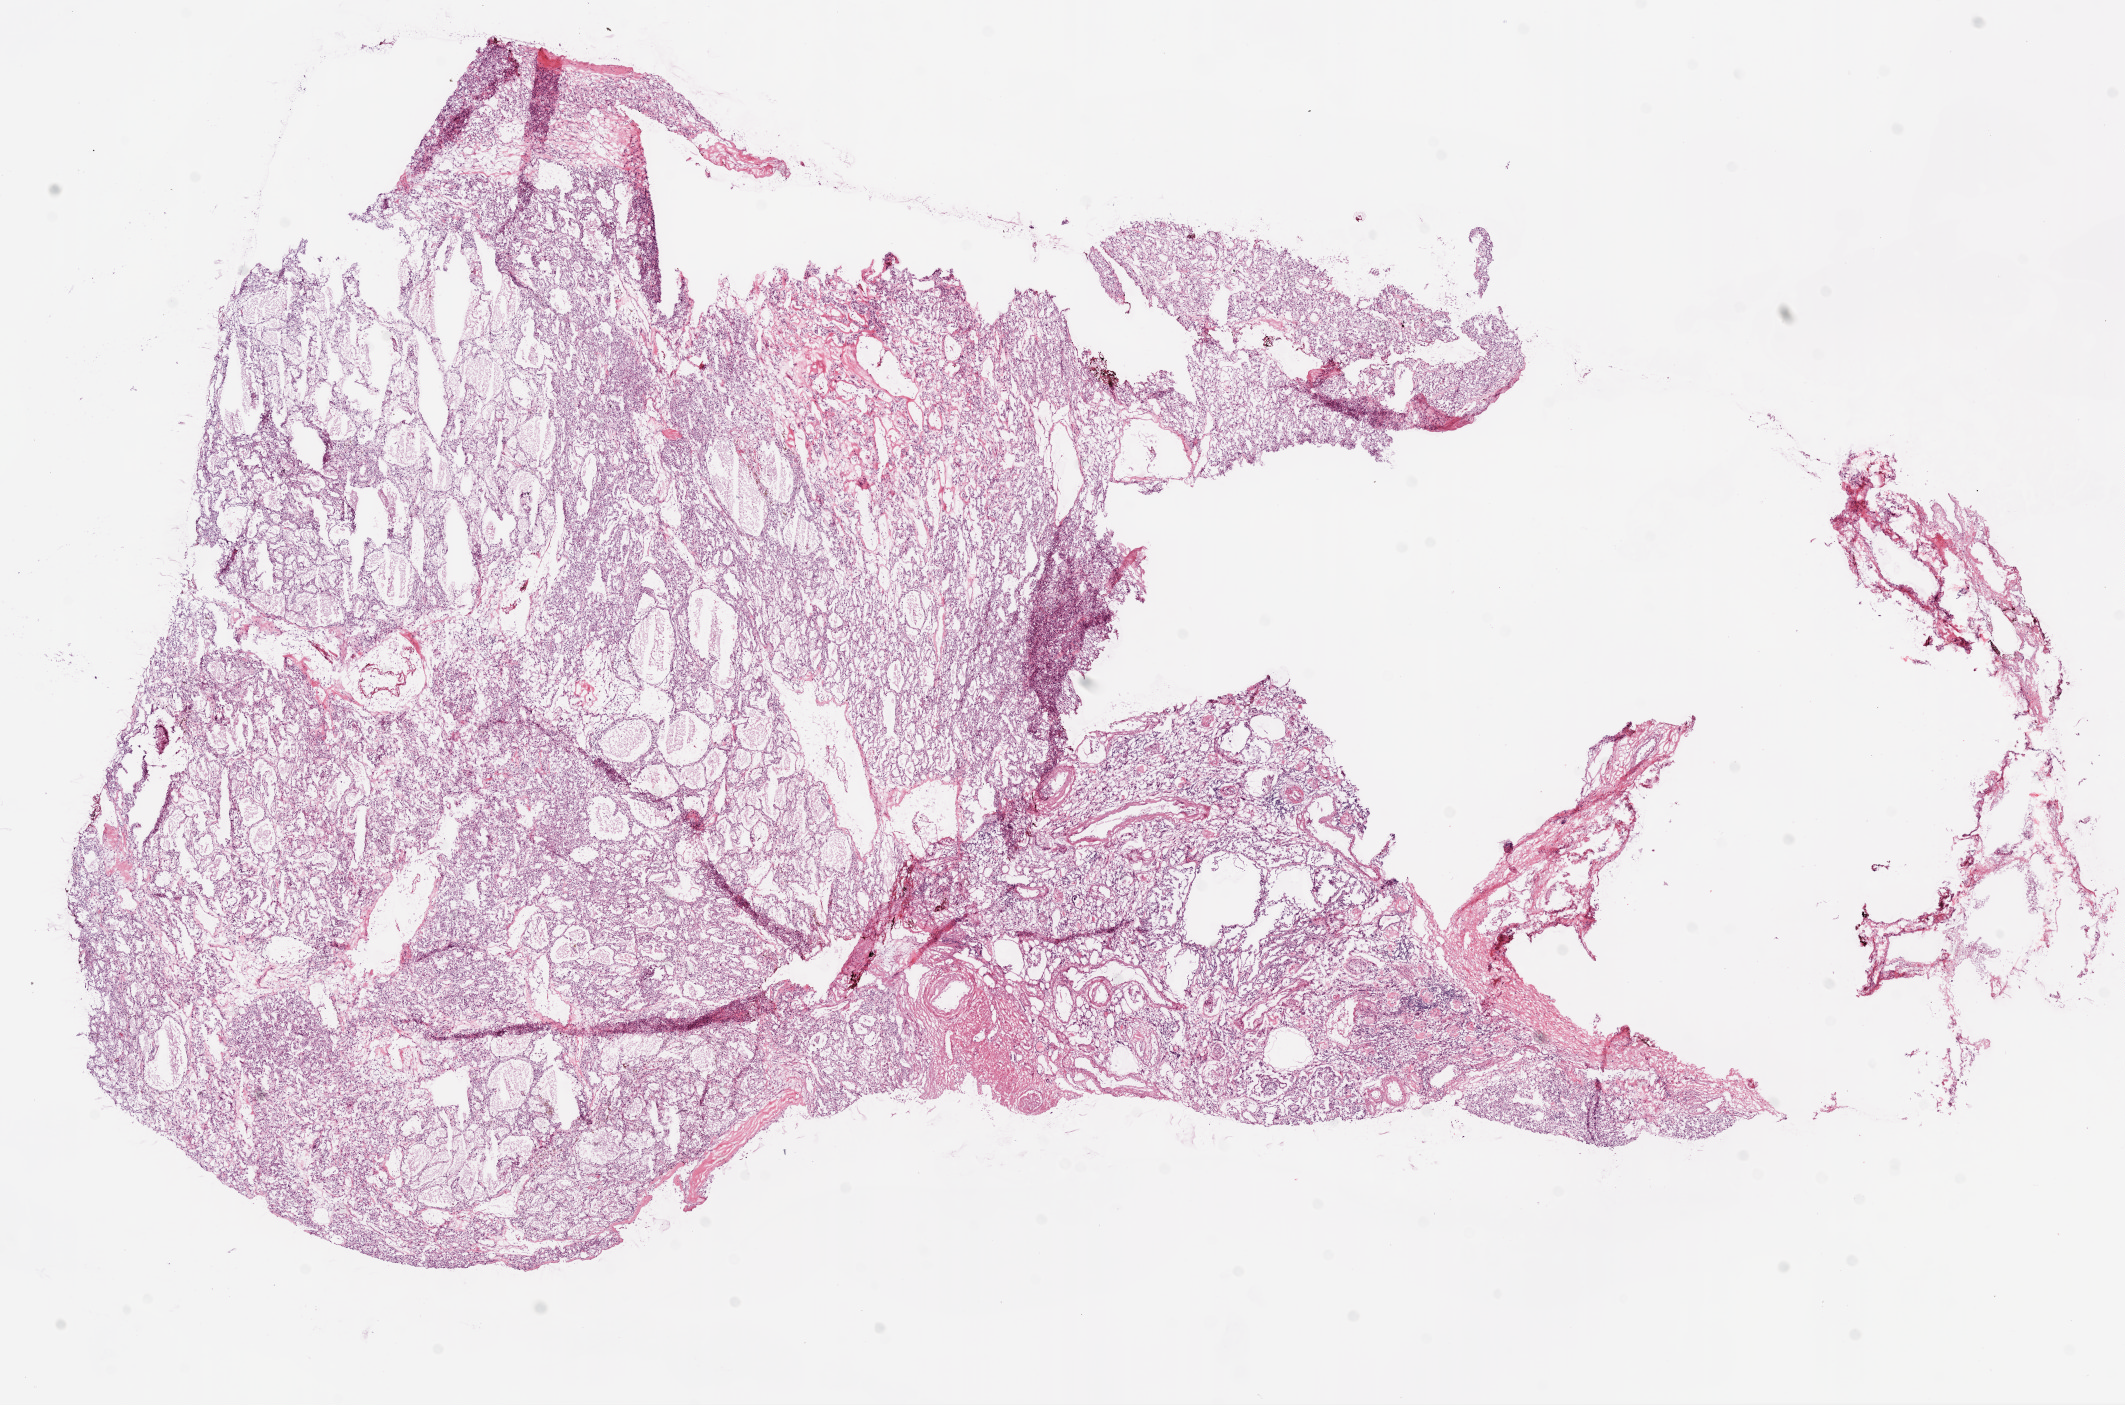
Whole-slide histology image, H&E-stained — low-resolution overview of the scanned area, about 17.1 x 11.3 mm (from a 20x scan), frozen section from the bottom of the tissue portion, kidney, primary tumour sample. Female, age 75 years at initial diagnosis. Histologic grade: G2 (moderately differentiated). Pathologist review of this section (percent, as recorded): tumour cells 85%, tumour nuclei 80%, normal cells 0%, stromal cells 15%, necrosis 0%.
TNM: T1a N0 M0. AJCC pathologic stage: I. Pathologic diagnosis: Clear cell adenocarcinoma, NOS.